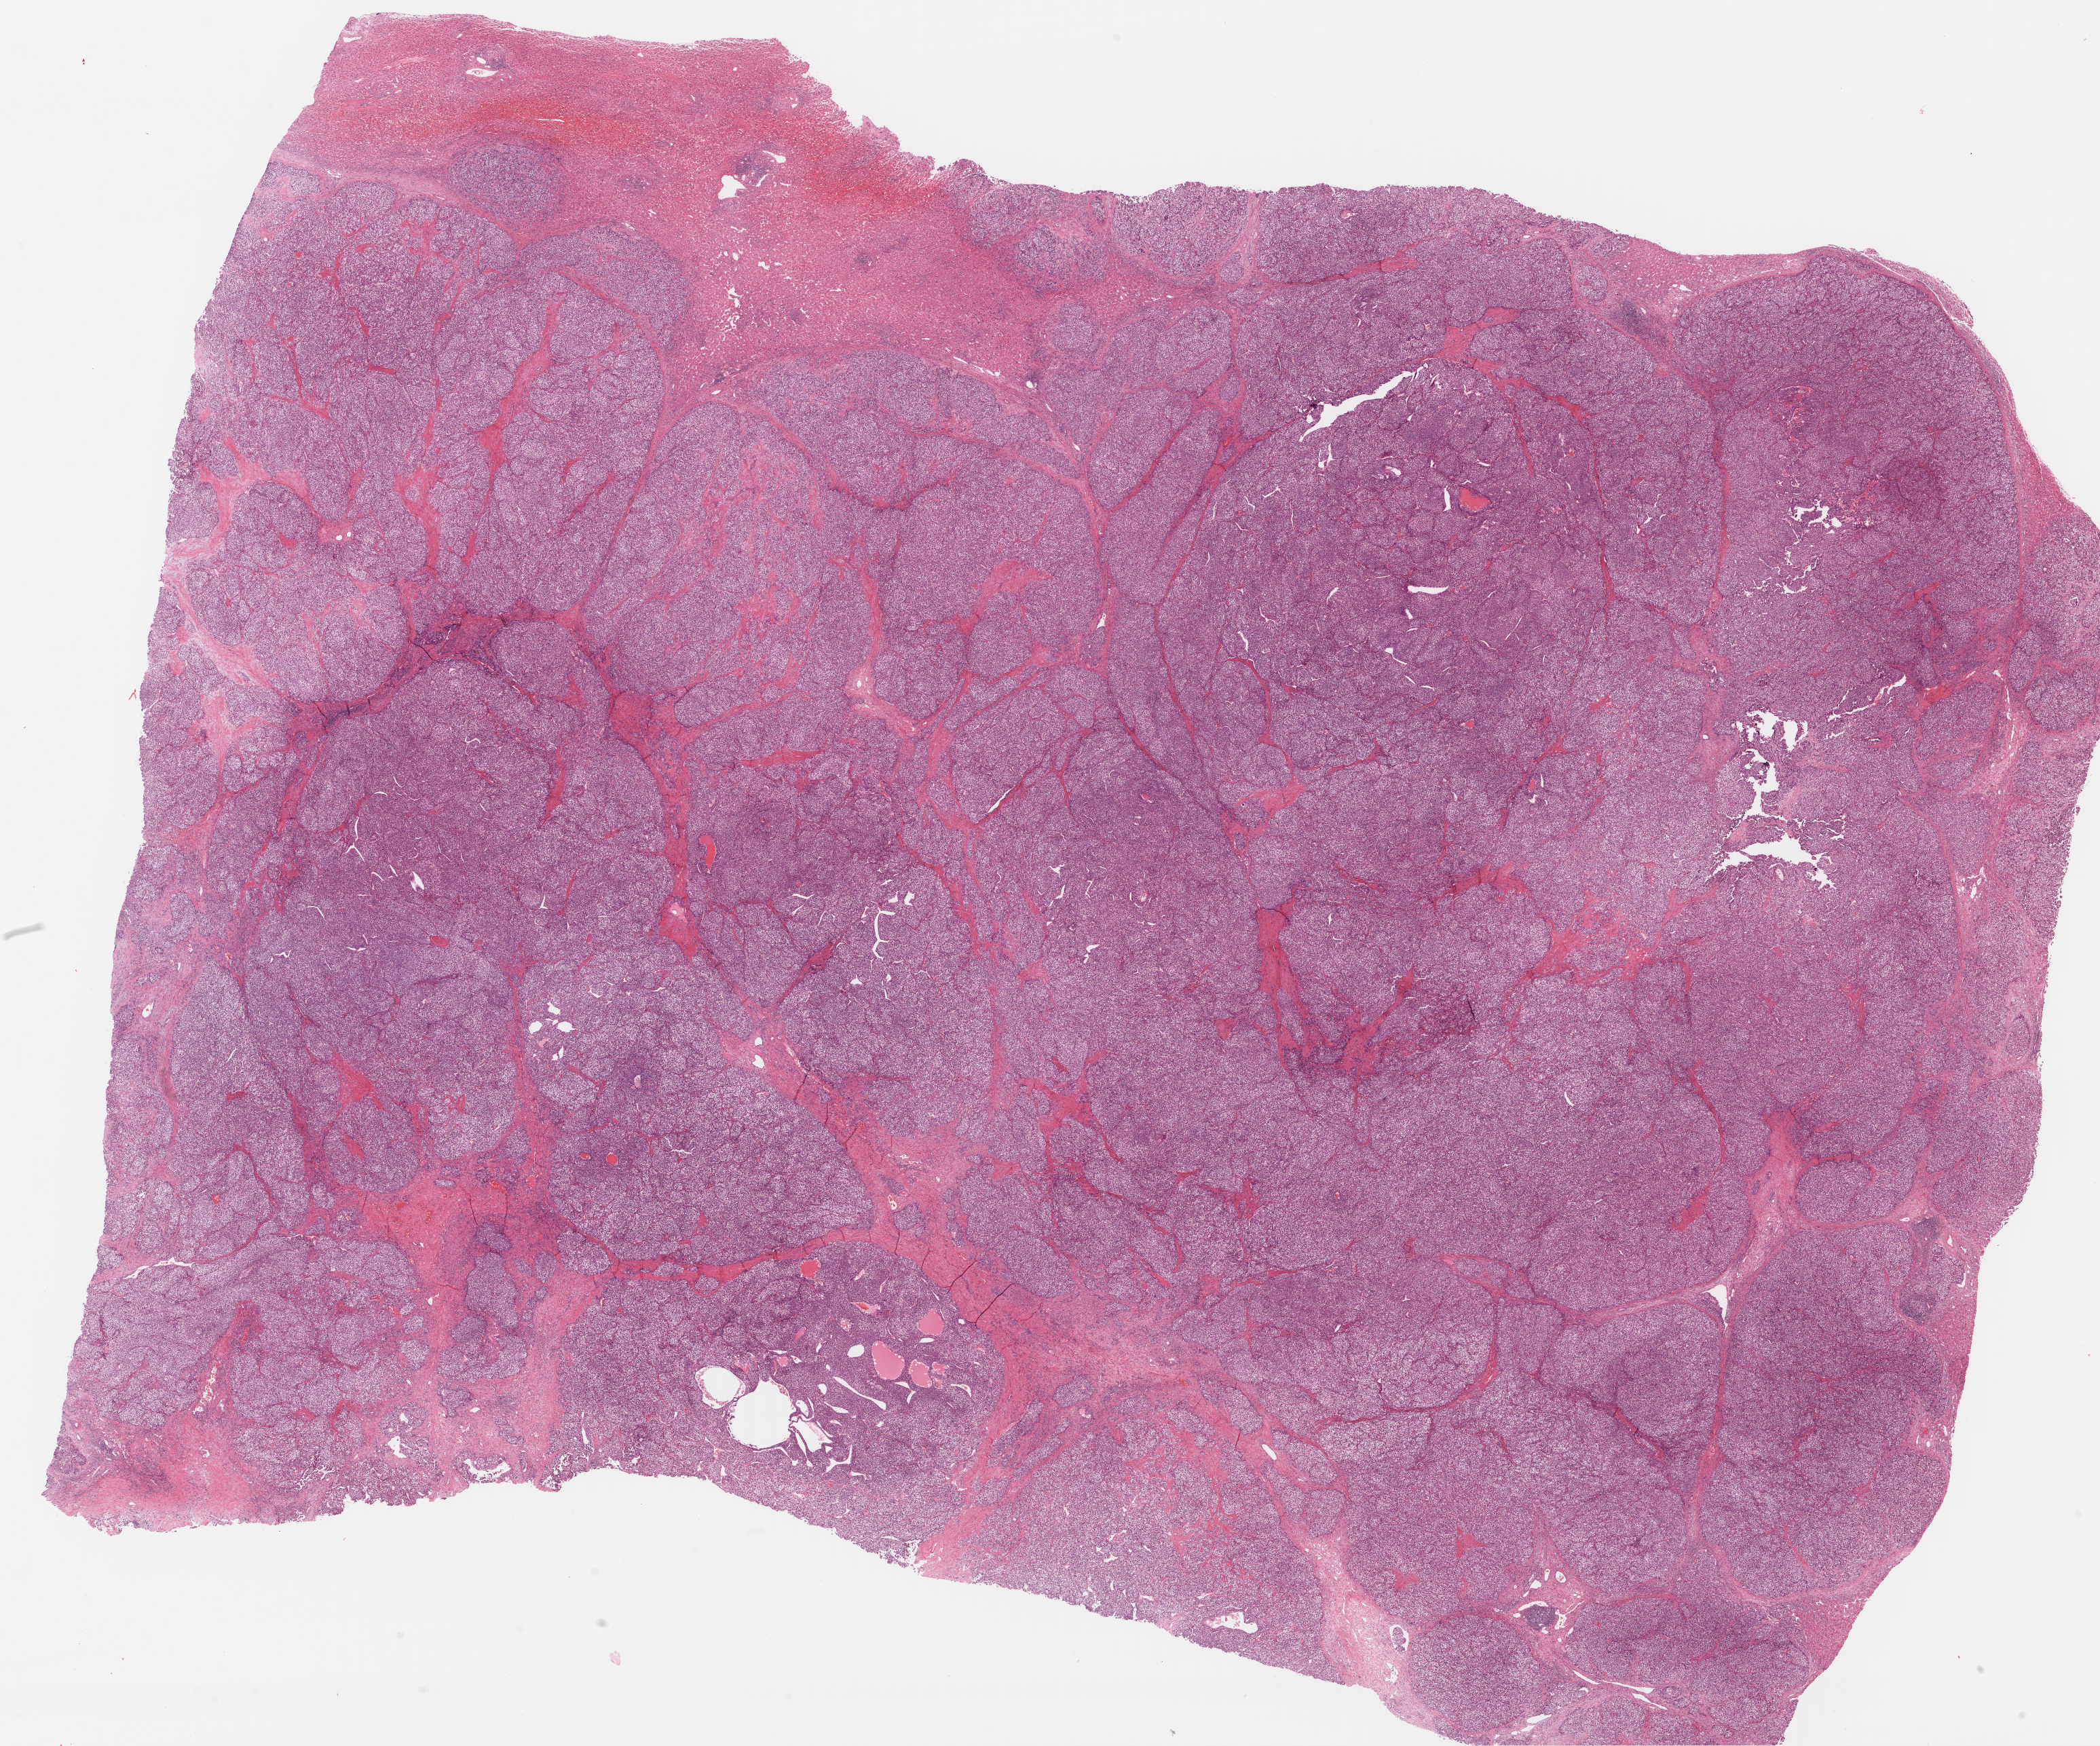
Whole-slide histology image, H&E — a low-resolution overview of the entire scanned area, about 24.3 x 20.2 mm (from a 40x scan), formalin-fixed paraffin-embedded (FFPE) diagnostic section, liver, primary tumour sample. Female, age 51 years at initial diagnosis. Histologic grade: G3 (poorly differentiated).
Histologic diagnosis: Hepatocellular carcinoma, NOS. AJCC pathologic stage: IIIA (7th edition).